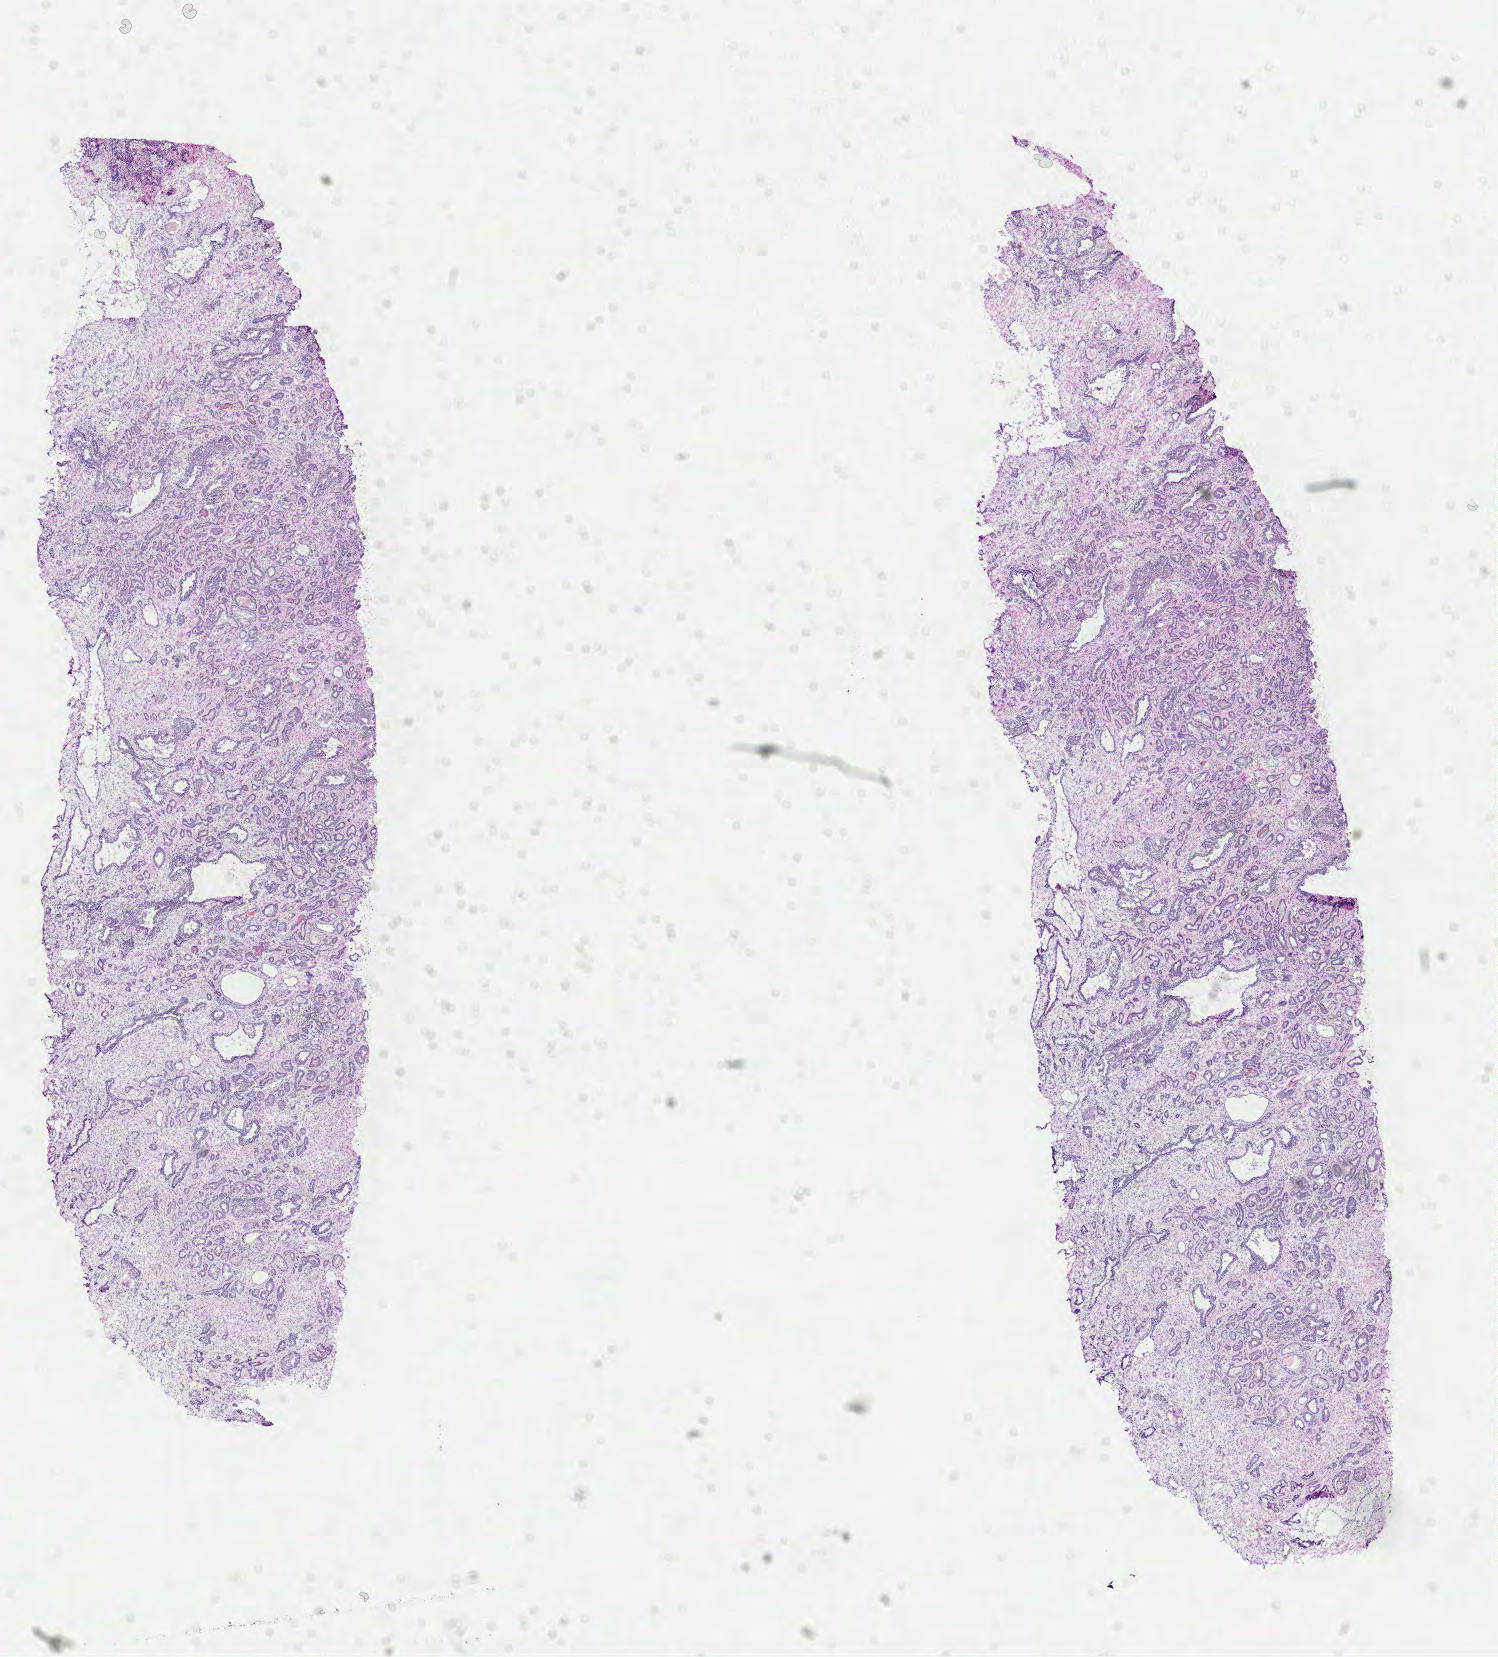
Digitized H&E tissue section (whole slide) — a low-resolution overview of the entire scanned area, about 12.1 x 13.4 mm (from a 40x scan). Formalin-fixed paraffin-embedded (FFPE) diagnostic section. Primary tumour sample from the prostate. Male, age 72 years at initial diagnosis. Gleason score: 6 (3+3).
- pathologic diagnosis: Acinar cell carcinoma (prostate gland)